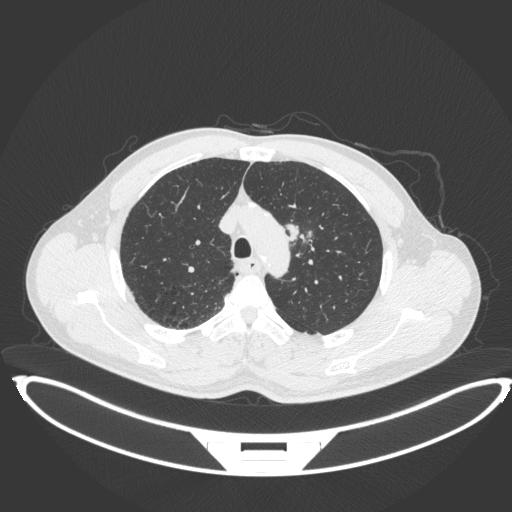
Chest CT, one axial slice; position 330 of 407 along the scan axis; reconstruction kernel B31f; lung window (W 1500 / L -600 HU); 1 mm slice thickness; 512 × 512 image matrix. Patient: male, 60 years. From the clinical record (not read from this slice): clinical TNM (as recorded): T2a N0 M0; histopathological grade: G1-G2.
Outlined on this slice (rectangle marked by the reading radiologist):
- lung tumour (recorded histology: squamous cell carcinoma): bounding box (x1, y1, x2, y2) in pixels: (286, 218, 302, 246)